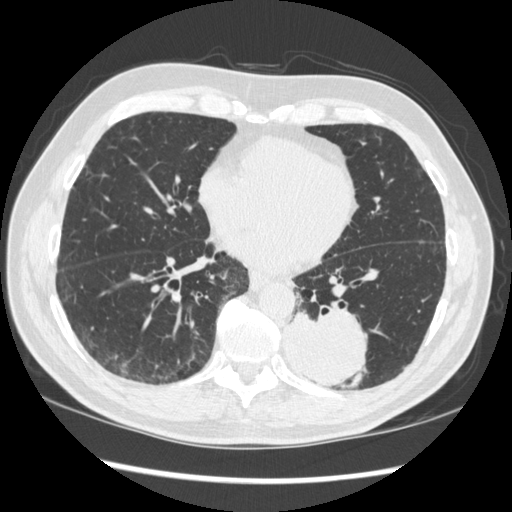
Low-dose screening chest CT, axial slice, first (baseline) screen, lung window (W 1500 / L -600 HU), 1.25 mm slice thickness, standard (soft-tissue) reconstruction kernel (STANDARD), slice 129 of 348 in the series. Male participant, aged 72 years at enrolment.
- Expert-annotated lung lesion, bounding box <272,298,376,387> (left, top, right, bottom; pixels).
- The screening reader recorded 2 non-calcified nodules or masses ≥4 mm on this exam; which of them this box marks is not recorded.
- Official screen result: positive, change unspecified: nodule(s) >= 4 mm or enlarging nodule(s), mass(es), or other non-specific abnormalities suspicious for lung cancer.
- Participant outcome: lung cancer diagnosed 37 days after this screen — squamous cell carcinoma, NOS, left lower lobe, stage IIIA (AJCC 6th edition), 60 mm at pathology.